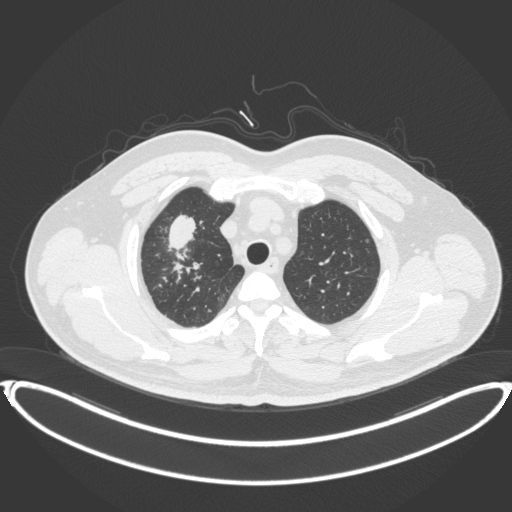
Chest CT, one axial slice; slice 318 of 399 in the series (ordered by position); reconstruction kernel B31f; 120 kVp; lung window (W 1500 / L -600 HU); 1 mm slice thickness; 512 × 512 image matrix, field of view 445 × 445 mm. Male patient, age 53 years. Case-level facts recorded for this patient, not image findings: clinical TNM (as recorded): T2a N0 M0.
Annotated regions visible in this slice (rectangle marked by the reading radiologist):
- lung tumour (recorded histology: adenocarcinoma): bounding box (x1, y1, x2, y2) in pixels: (167, 206, 198, 255)